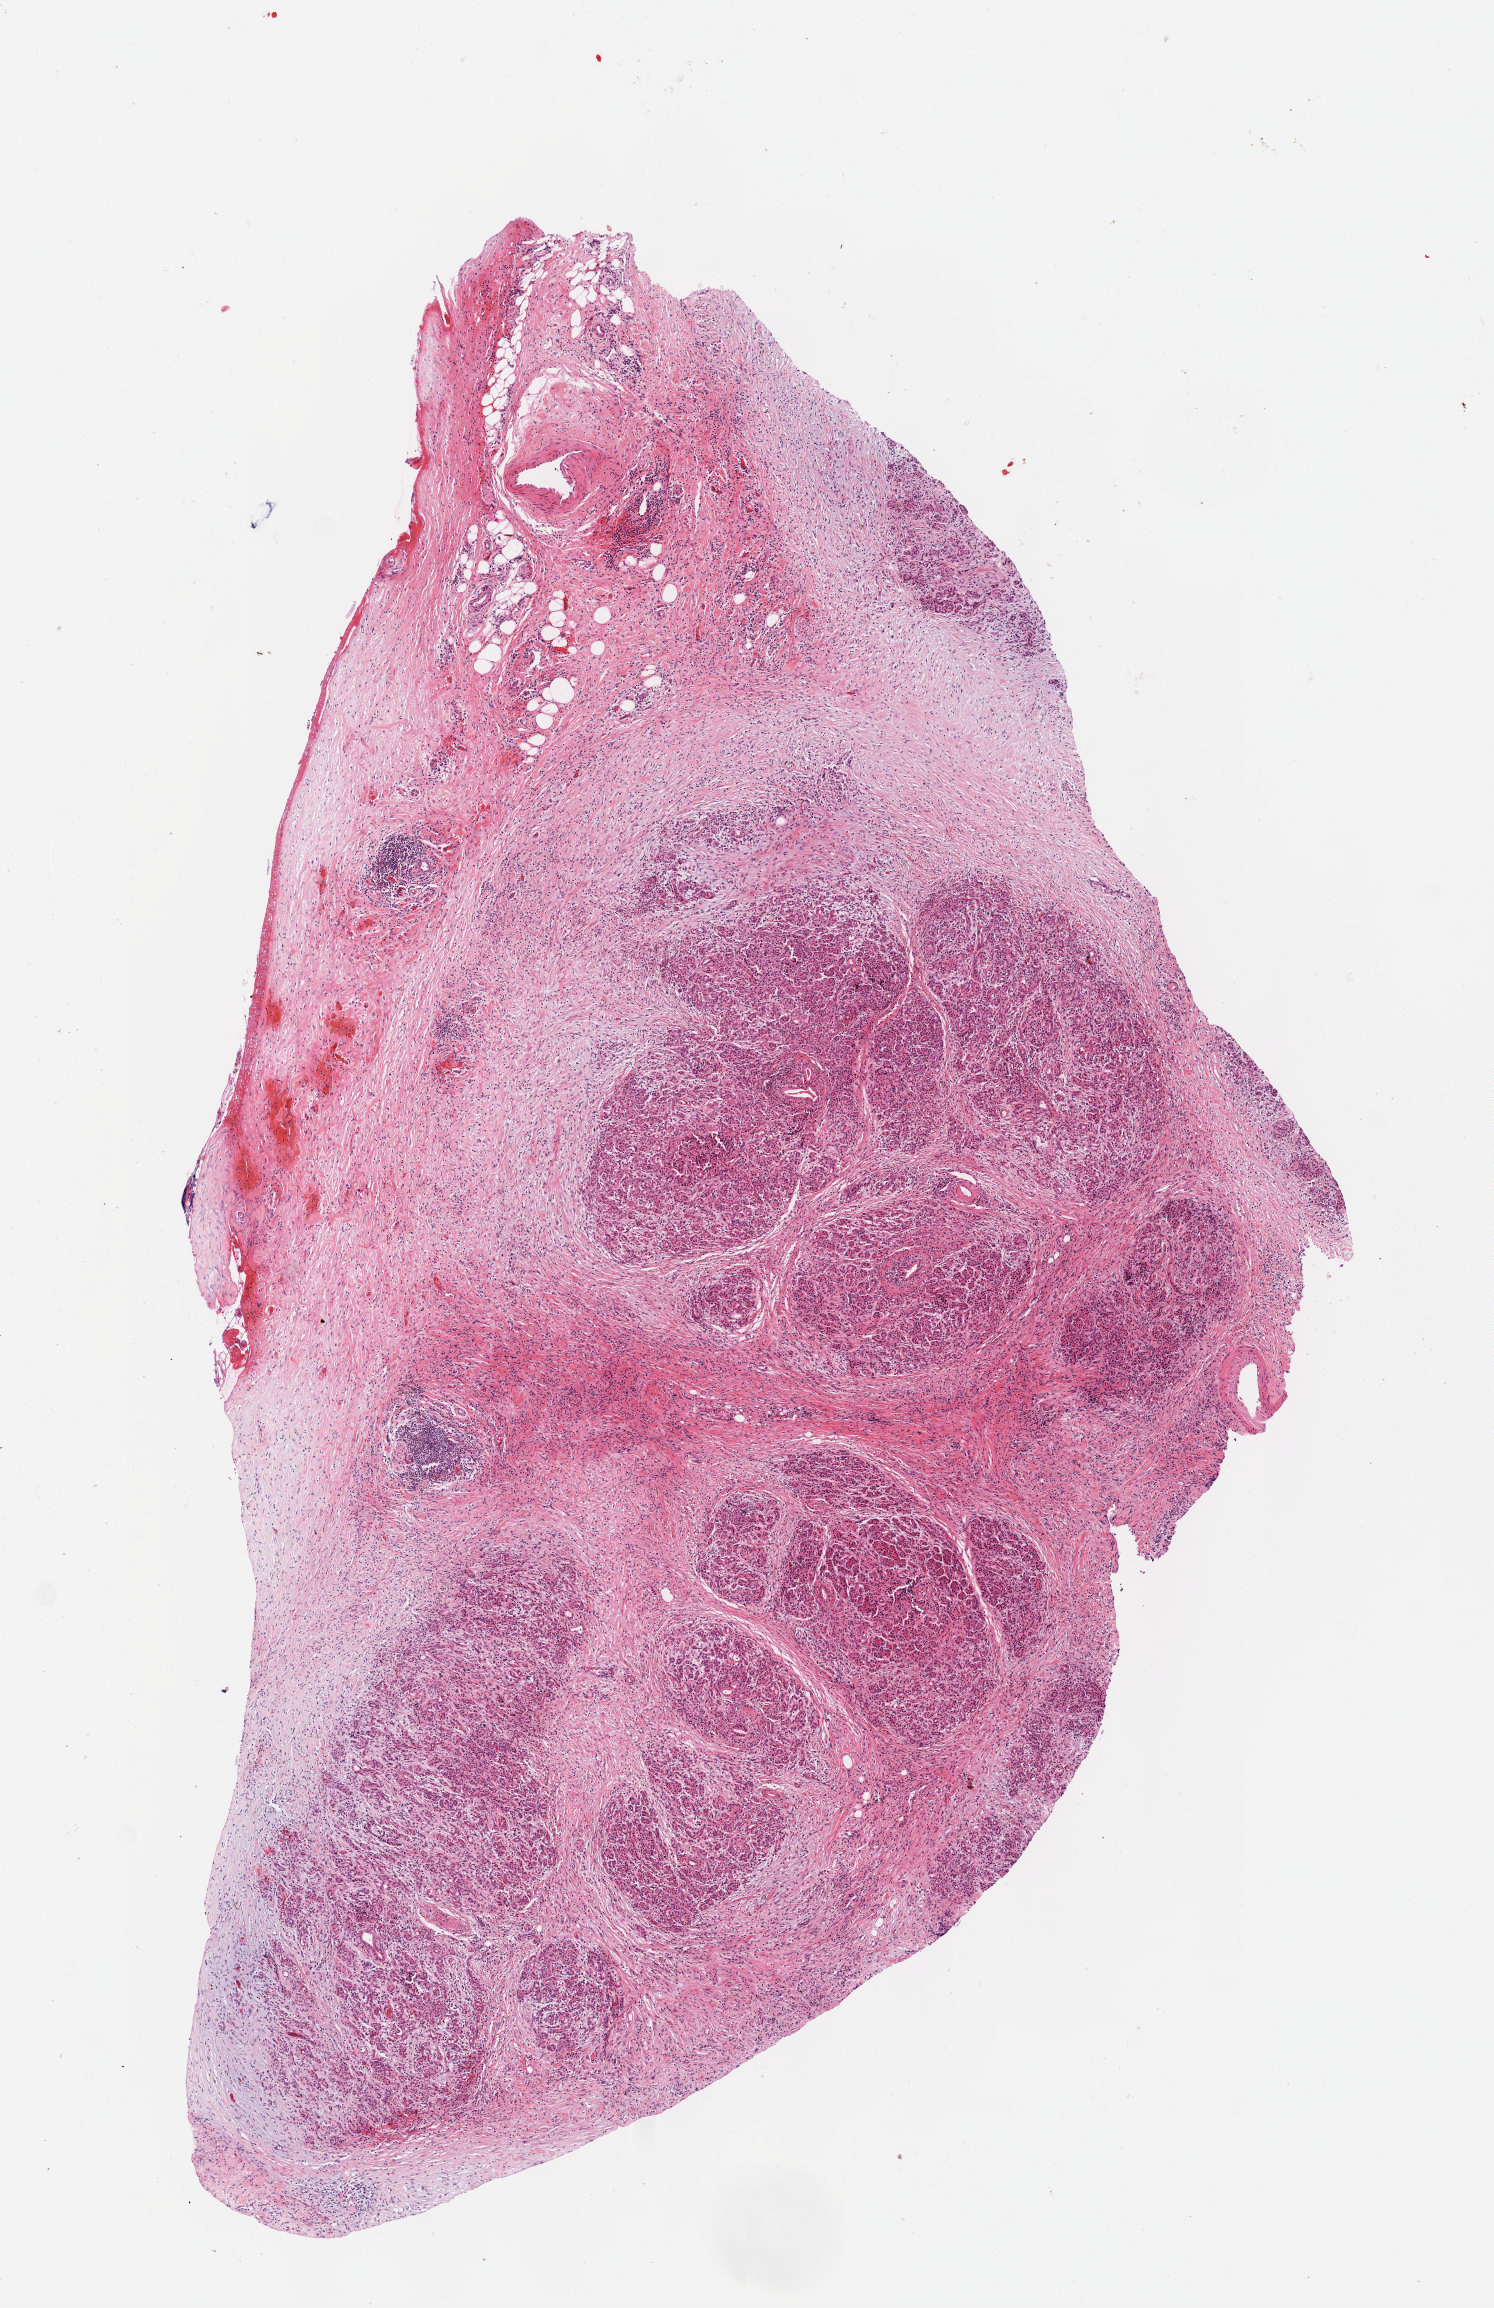
H&E-stained whole-slide image — a low-resolution overview of the entire scanned area, about 6.0 x 9.3 mm (slide scanned at 40x). Formalin-fixed paraffin-embedded (FFPE) diagnostic section. Solid tissue normal (non-tumour tissue) sample from the pancreas. Patient: female, age at initial diagnosis 61 years.
This section: solid tissue normal (non-tumour) sample from the same patient. Patient diagnosis: Infiltrating duct carcinoma, NOS (head of pancreas).